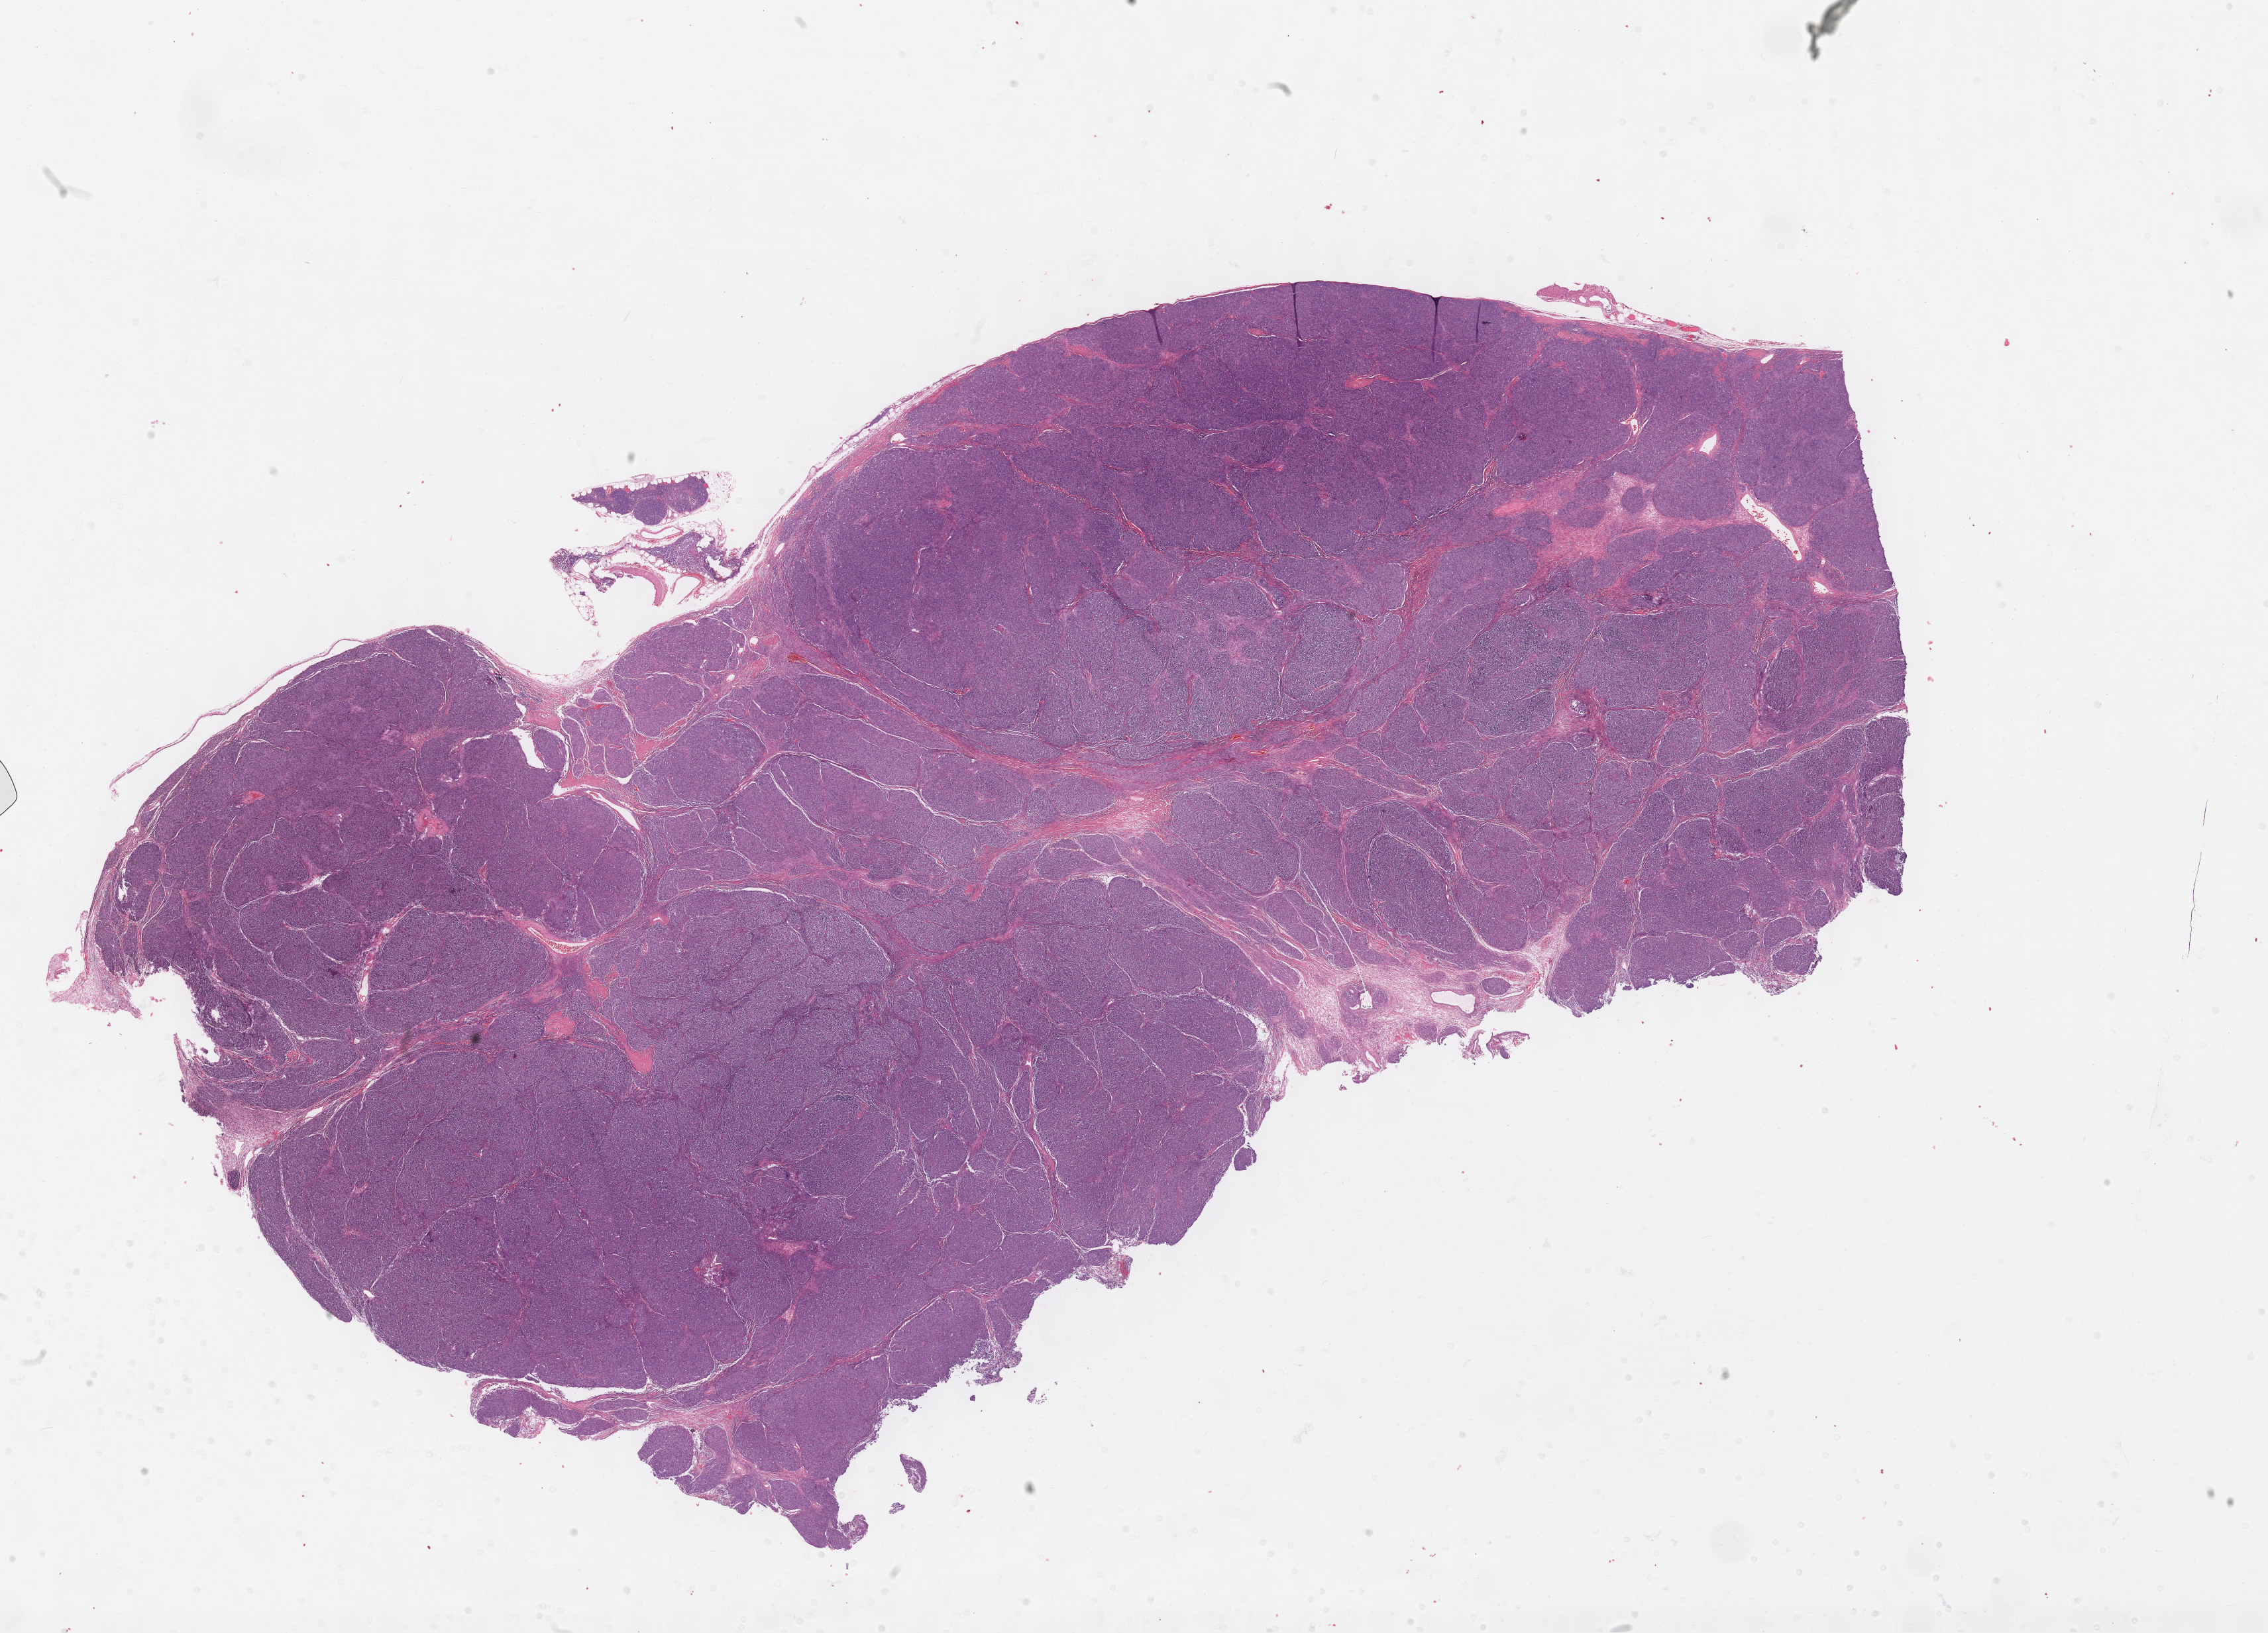
Digitized H&E tissue section (whole slide), shown as a low-resolution overview of the whole scanned area (about 27.7 x 19.9 mm, slide scanned at 40x); FFPE section; primary tumour sample from the thymus. Male patient; age at initial diagnosis 41 years.
Pathologic diagnosis: Thymoma, type B2, malignant.